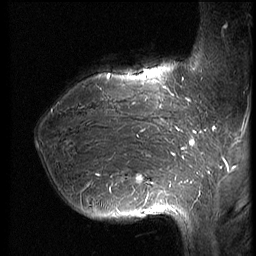
Breast MRI (dynamic contrast-enhanced), one sagittal slice. Slice 22 of 66 in the series (ordered by position). Dynamic contrast-enhanced series, image 2 of 3 at this slice position (ordered by acquisition). 1.5 T. TE 4.2 ms, TR 8.9 ms. 2.5 mm slice thickness. 256 × 256 image matrix, field of view 200 × 200 mm. Patient: female, 39 years. Case-level facts recorded for this patient, not image findings: setting: breast cancer imaged before/during neoadjuvant chemotherapy; receptor status: HER2-positive.
Outlined on this slice (semi-automatically segmented with operator editing):
- analysis volume of interest (the breast-tissue region the enhancement analysis was run in; not a lesion): bounding box [x1, y1, x2, y2] px = [34, 75, 188, 218]
- tumour enhancement mask (voxels above the 140 % enhancement threshold inside the analysis volume of interest): [108, 75, 187, 193]